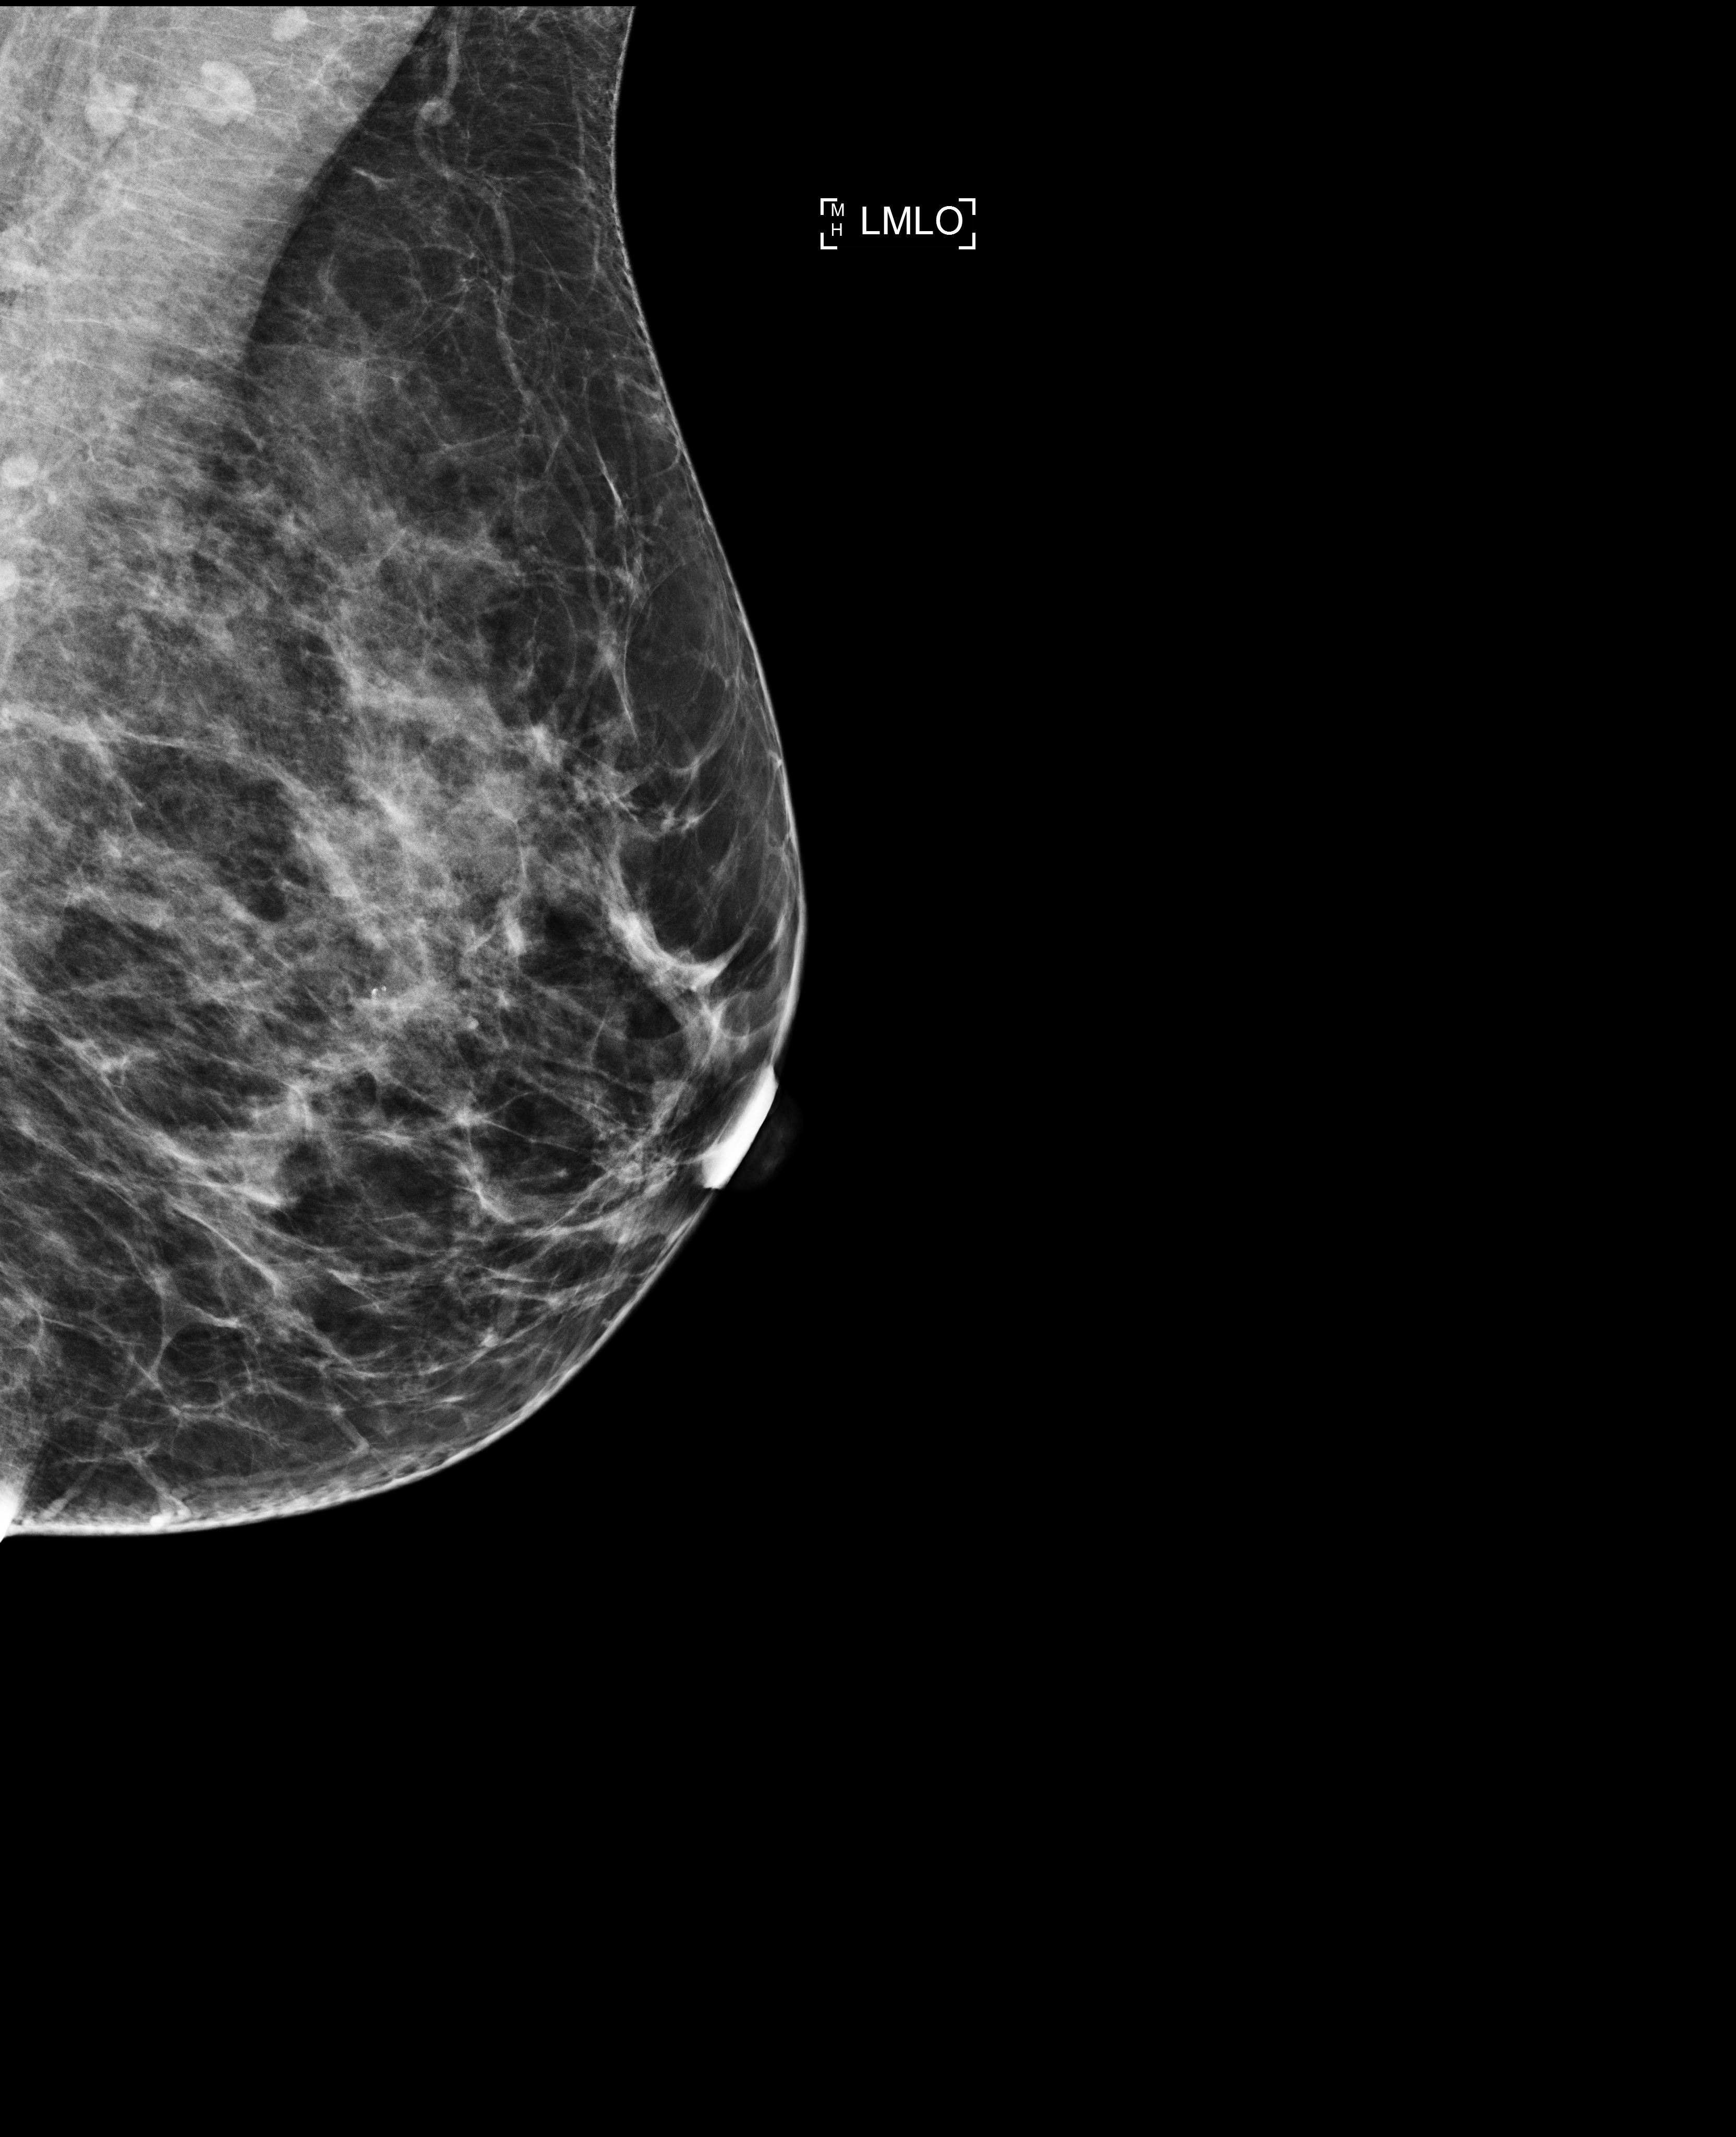
Annual screening mammography examination; compressed breast thickness 62 mm. Patient: female, 46 years.
Image type: full-field digital mammogram. Breast: left. Projection: mediolateral oblique (MLO) view. BI-RADS breast density category at the screening exam (both breasts, scale 1–4): 3. Final BI-RADS assessment for this screening round (tomosynthesis exam, both breasts): category 1. Recall: no recall after this screen.